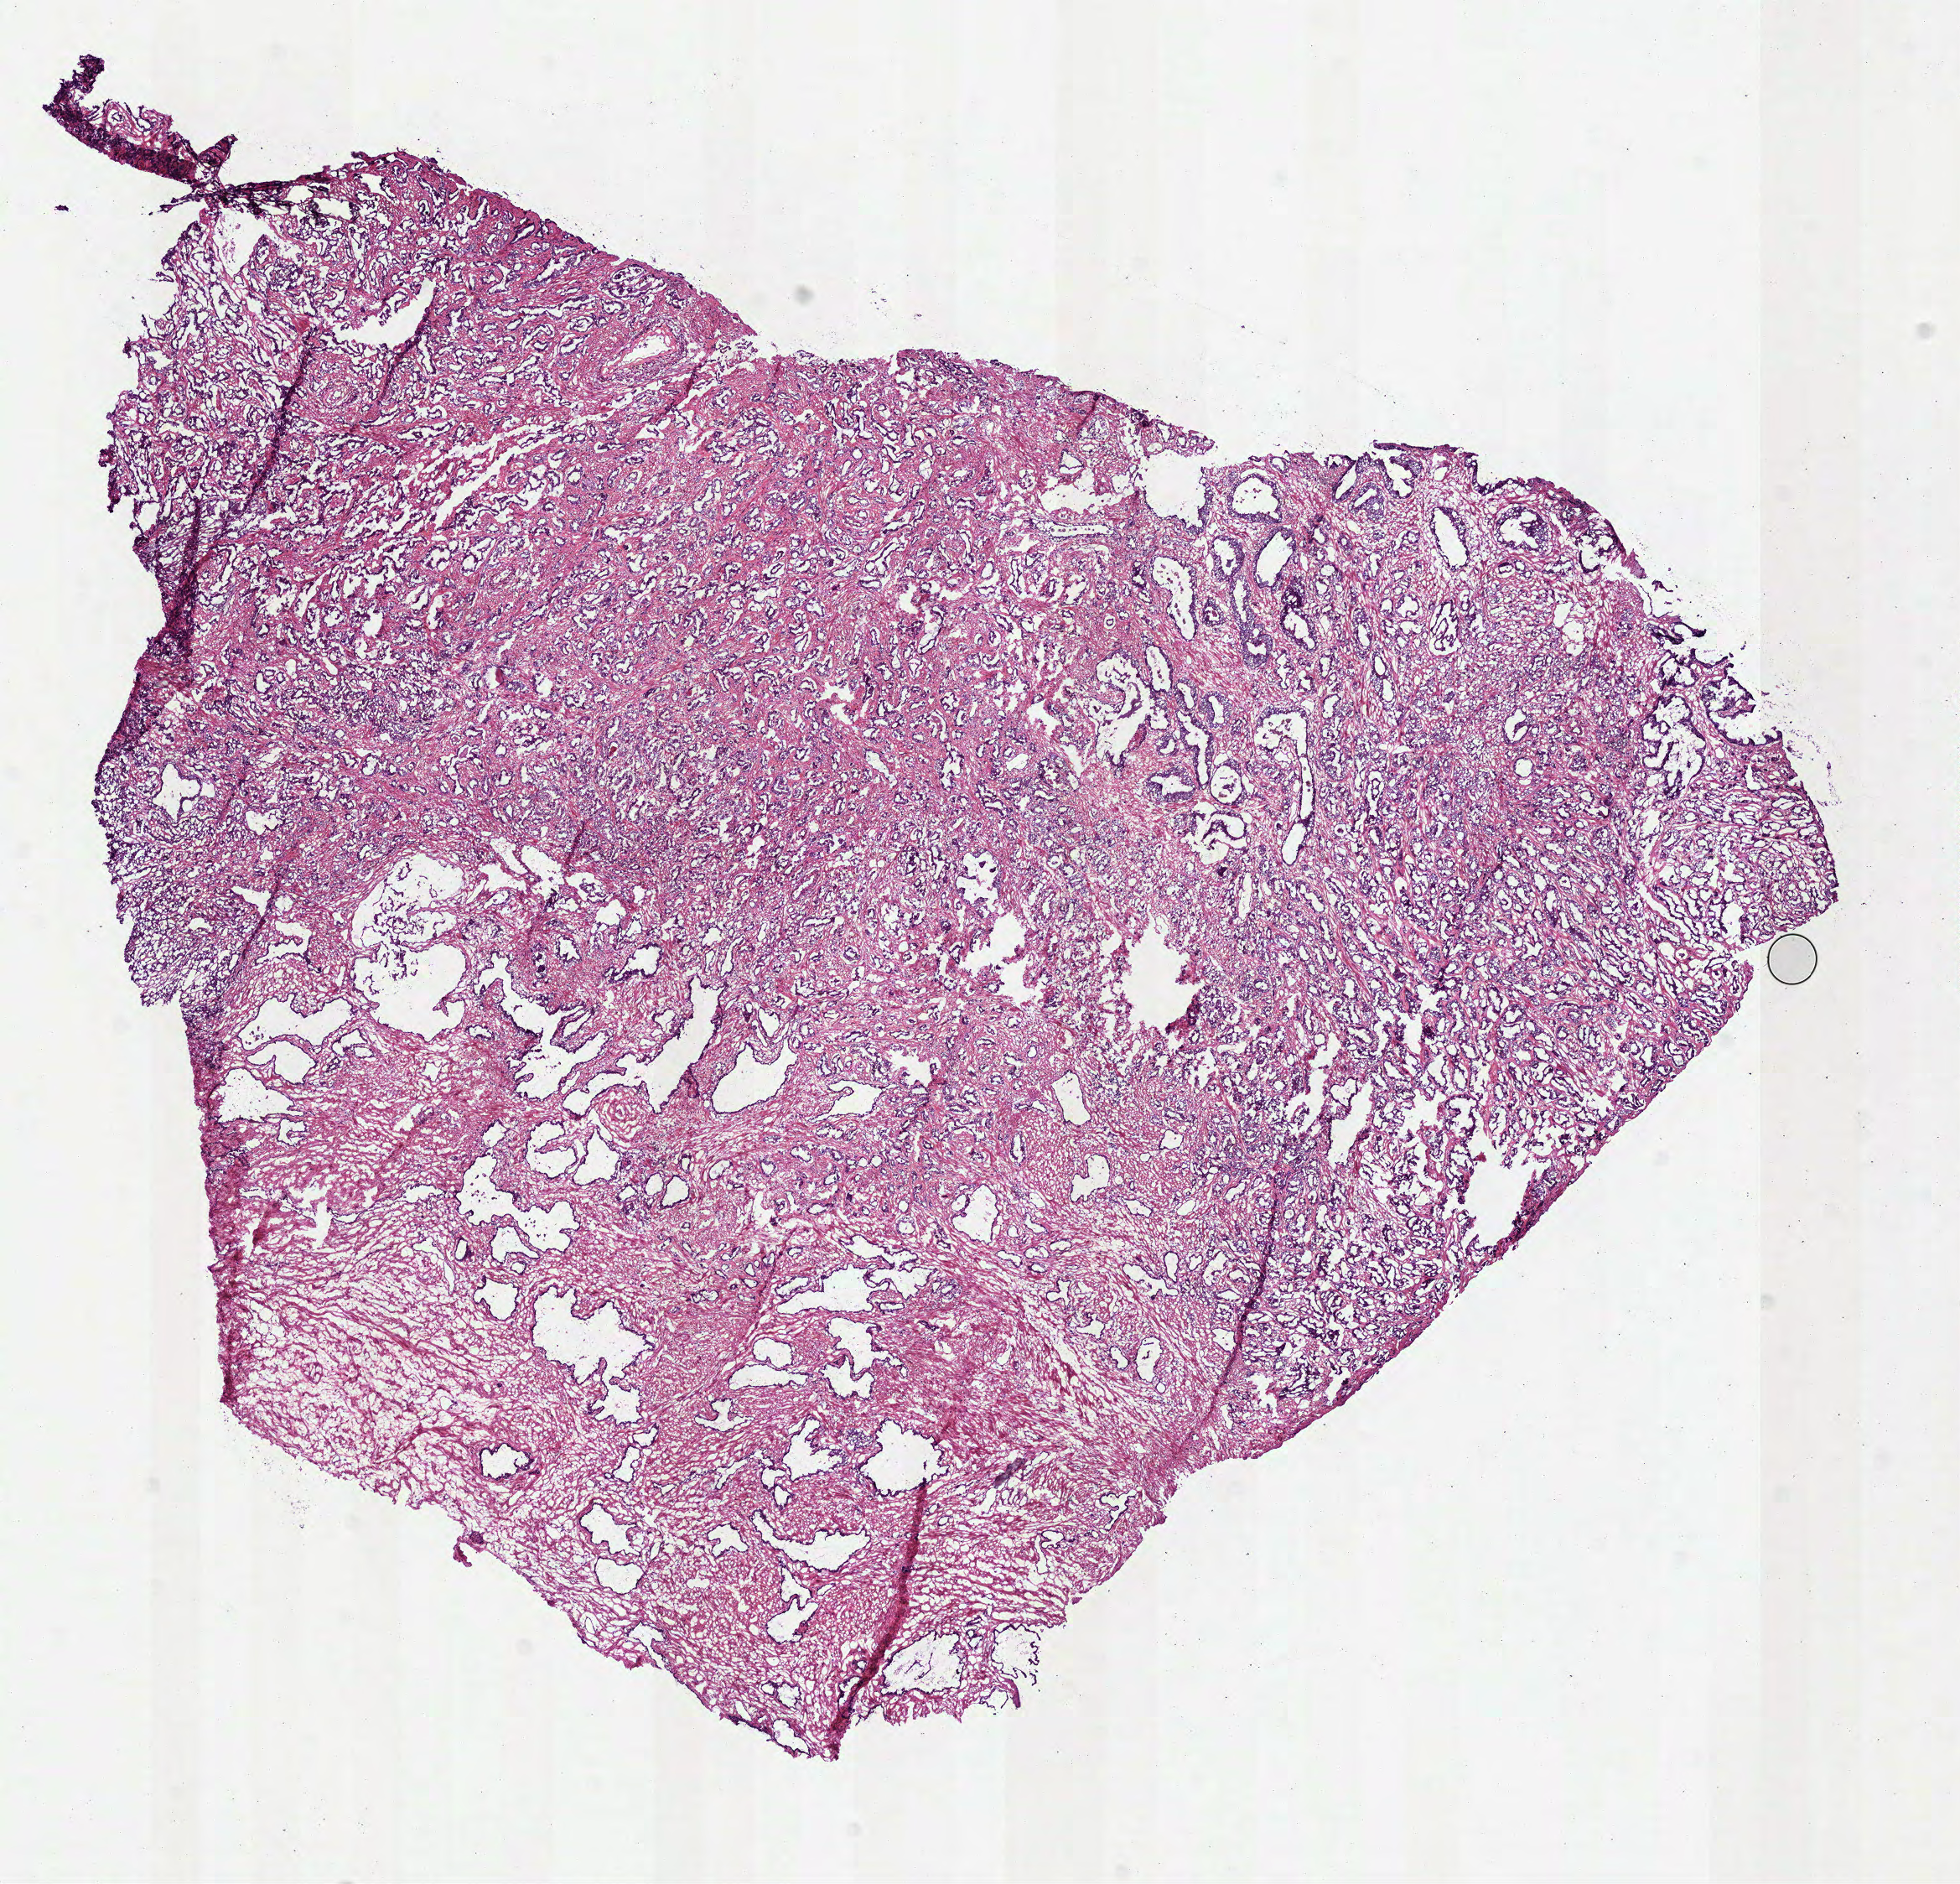
Digitized H&E-stained tissue section (whole slide), shown as a low-resolution overview of the whole scanned area (about 9.4 x 9.1 mm). Frozen section from the bottom of the tissue portion. Sample: primary tumour, prostate. Male patient; age at initial diagnosis 69 years. Gleason score: 8 (4+4). Composition of this section per pathologist review: tumour cells 60%, tumour nuclei 60%, normal cells 15%, stromal cells 25%, necrosis 0%.
- pathologic diagnosis: Acinar cell carcinoma
- laterality: bilateral
- lymph nodes positive (case pathology): 0 of 15 examined